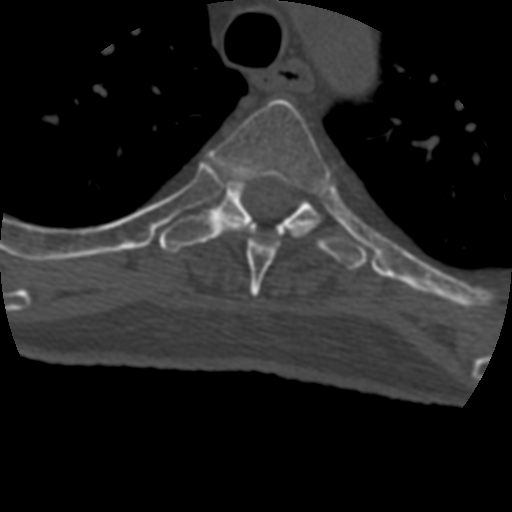
CT including the spine, one axial slice. Position 329 of 399 along the scan axis. Reconstruction kernel STANDARD. Bone window (W 1800 / L 400 HU). 1.25 mm slice thickness. 512 × 512 image matrix, field of view 160 × 160 mm. Patient age 69 years. From the clinical record (not read from this slice): primary cancer: prostate.
Annotated regions visible in this slice (semi-automatically segmented with operator editing):
- T4 vertebra: box from (x=209, y=99) to (x=330, y=298) px
- T5 vertebra: (x=159, y=178)–(x=370, y=270)